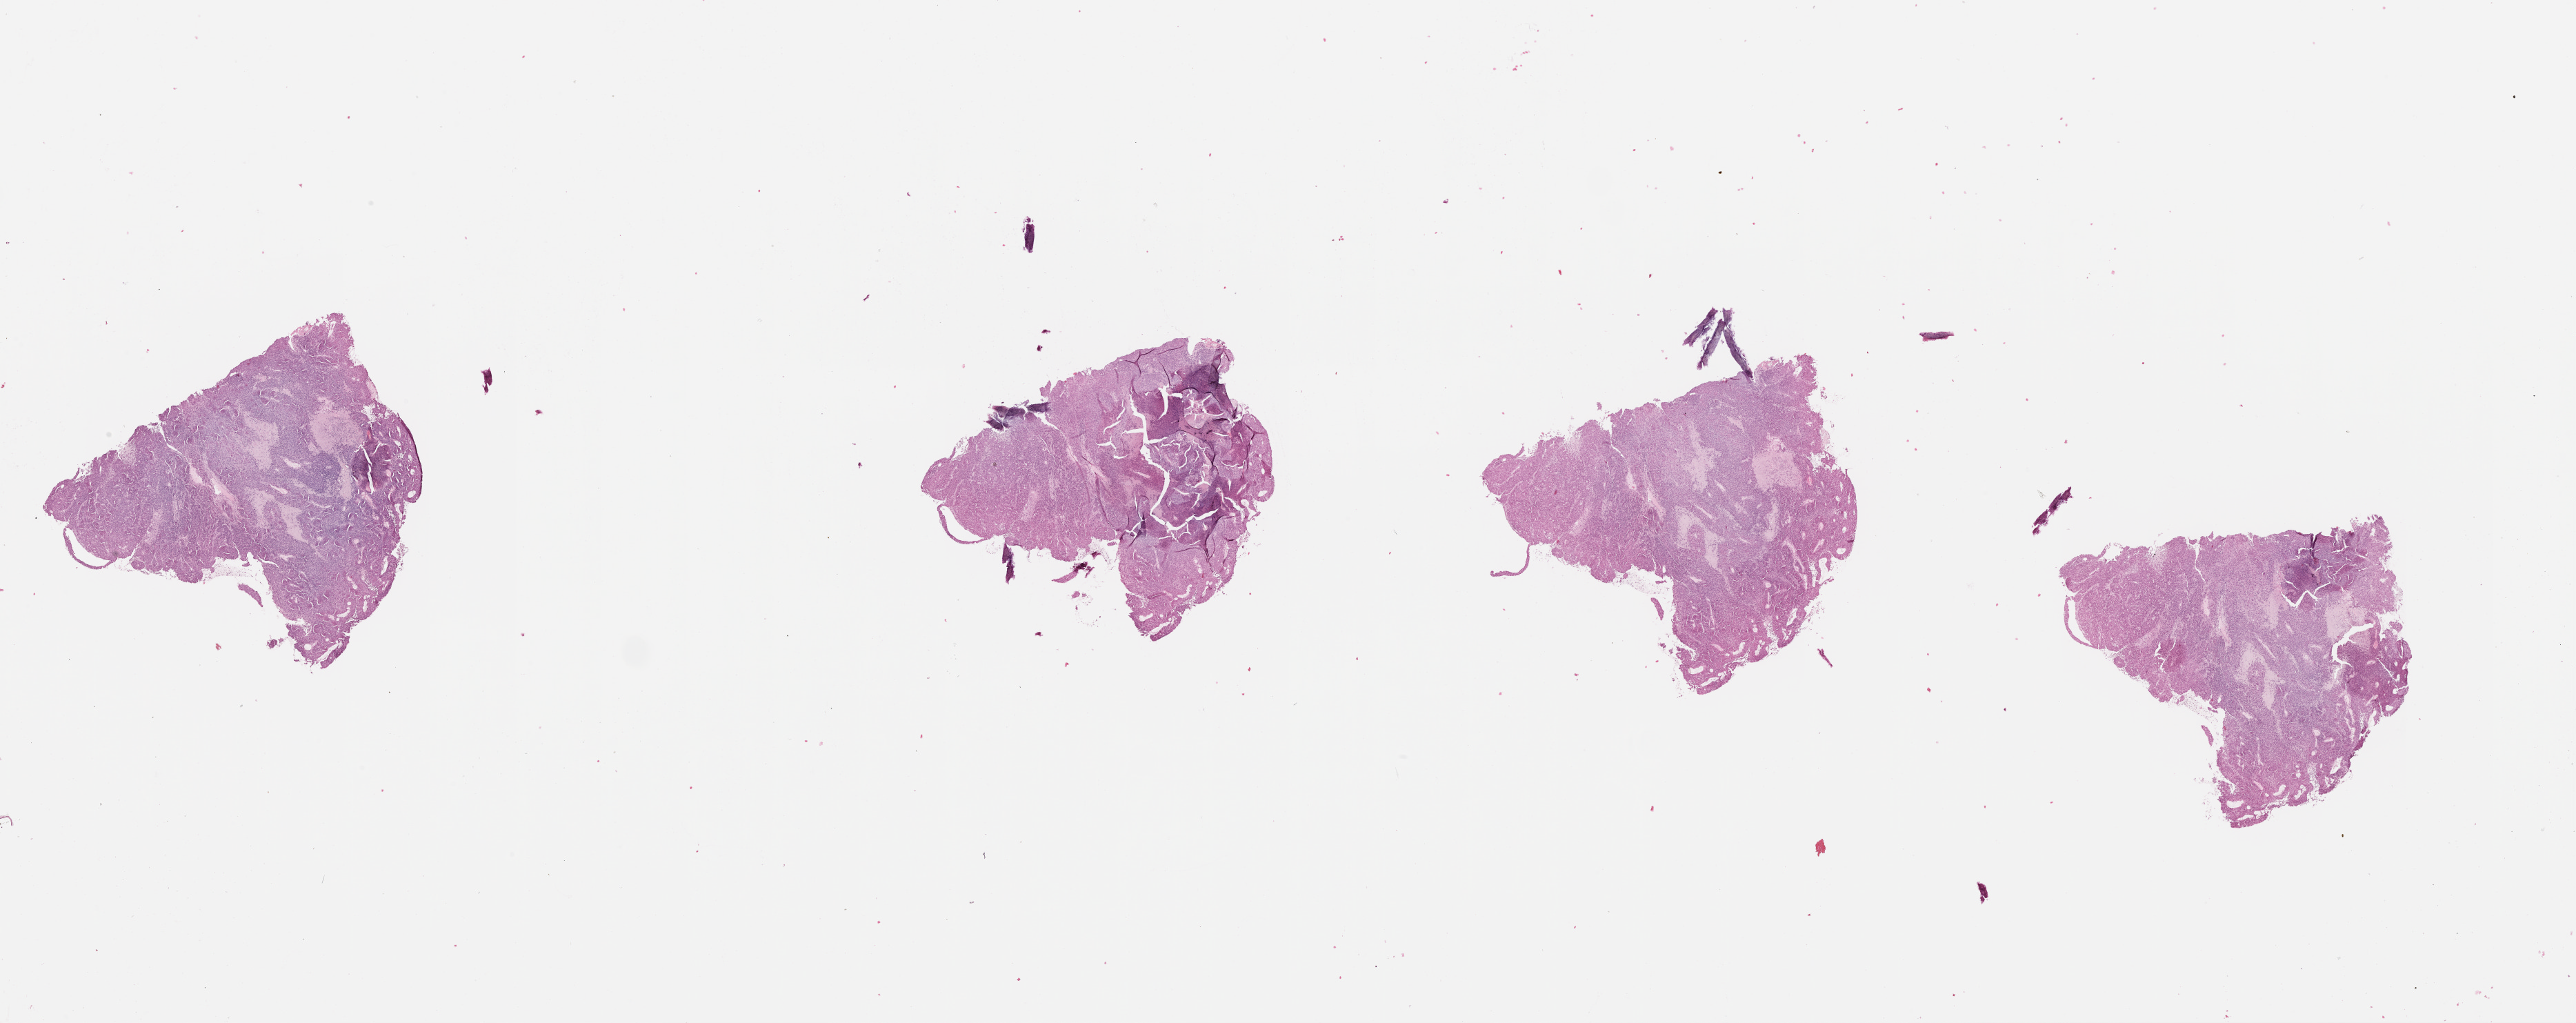
Digitized H&E tissue section (whole slide), a low-resolution overview of the entire scanned area, about 30.1 x 11.9 mm (from a 20x scan), tumour tissue sample, sampled site: uterus. Female, 85 y/o. Histologic grade: G3 (poorly differentiated). Slide review estimates, as recorded: tumour nuclei 80%, necrosis 0%.
* primary tumour site (as recorded): posterior endometrium
* AJCC pathologic stage: I
* histologic diagnosis: Endometrioid adenocarcinoma, NOS